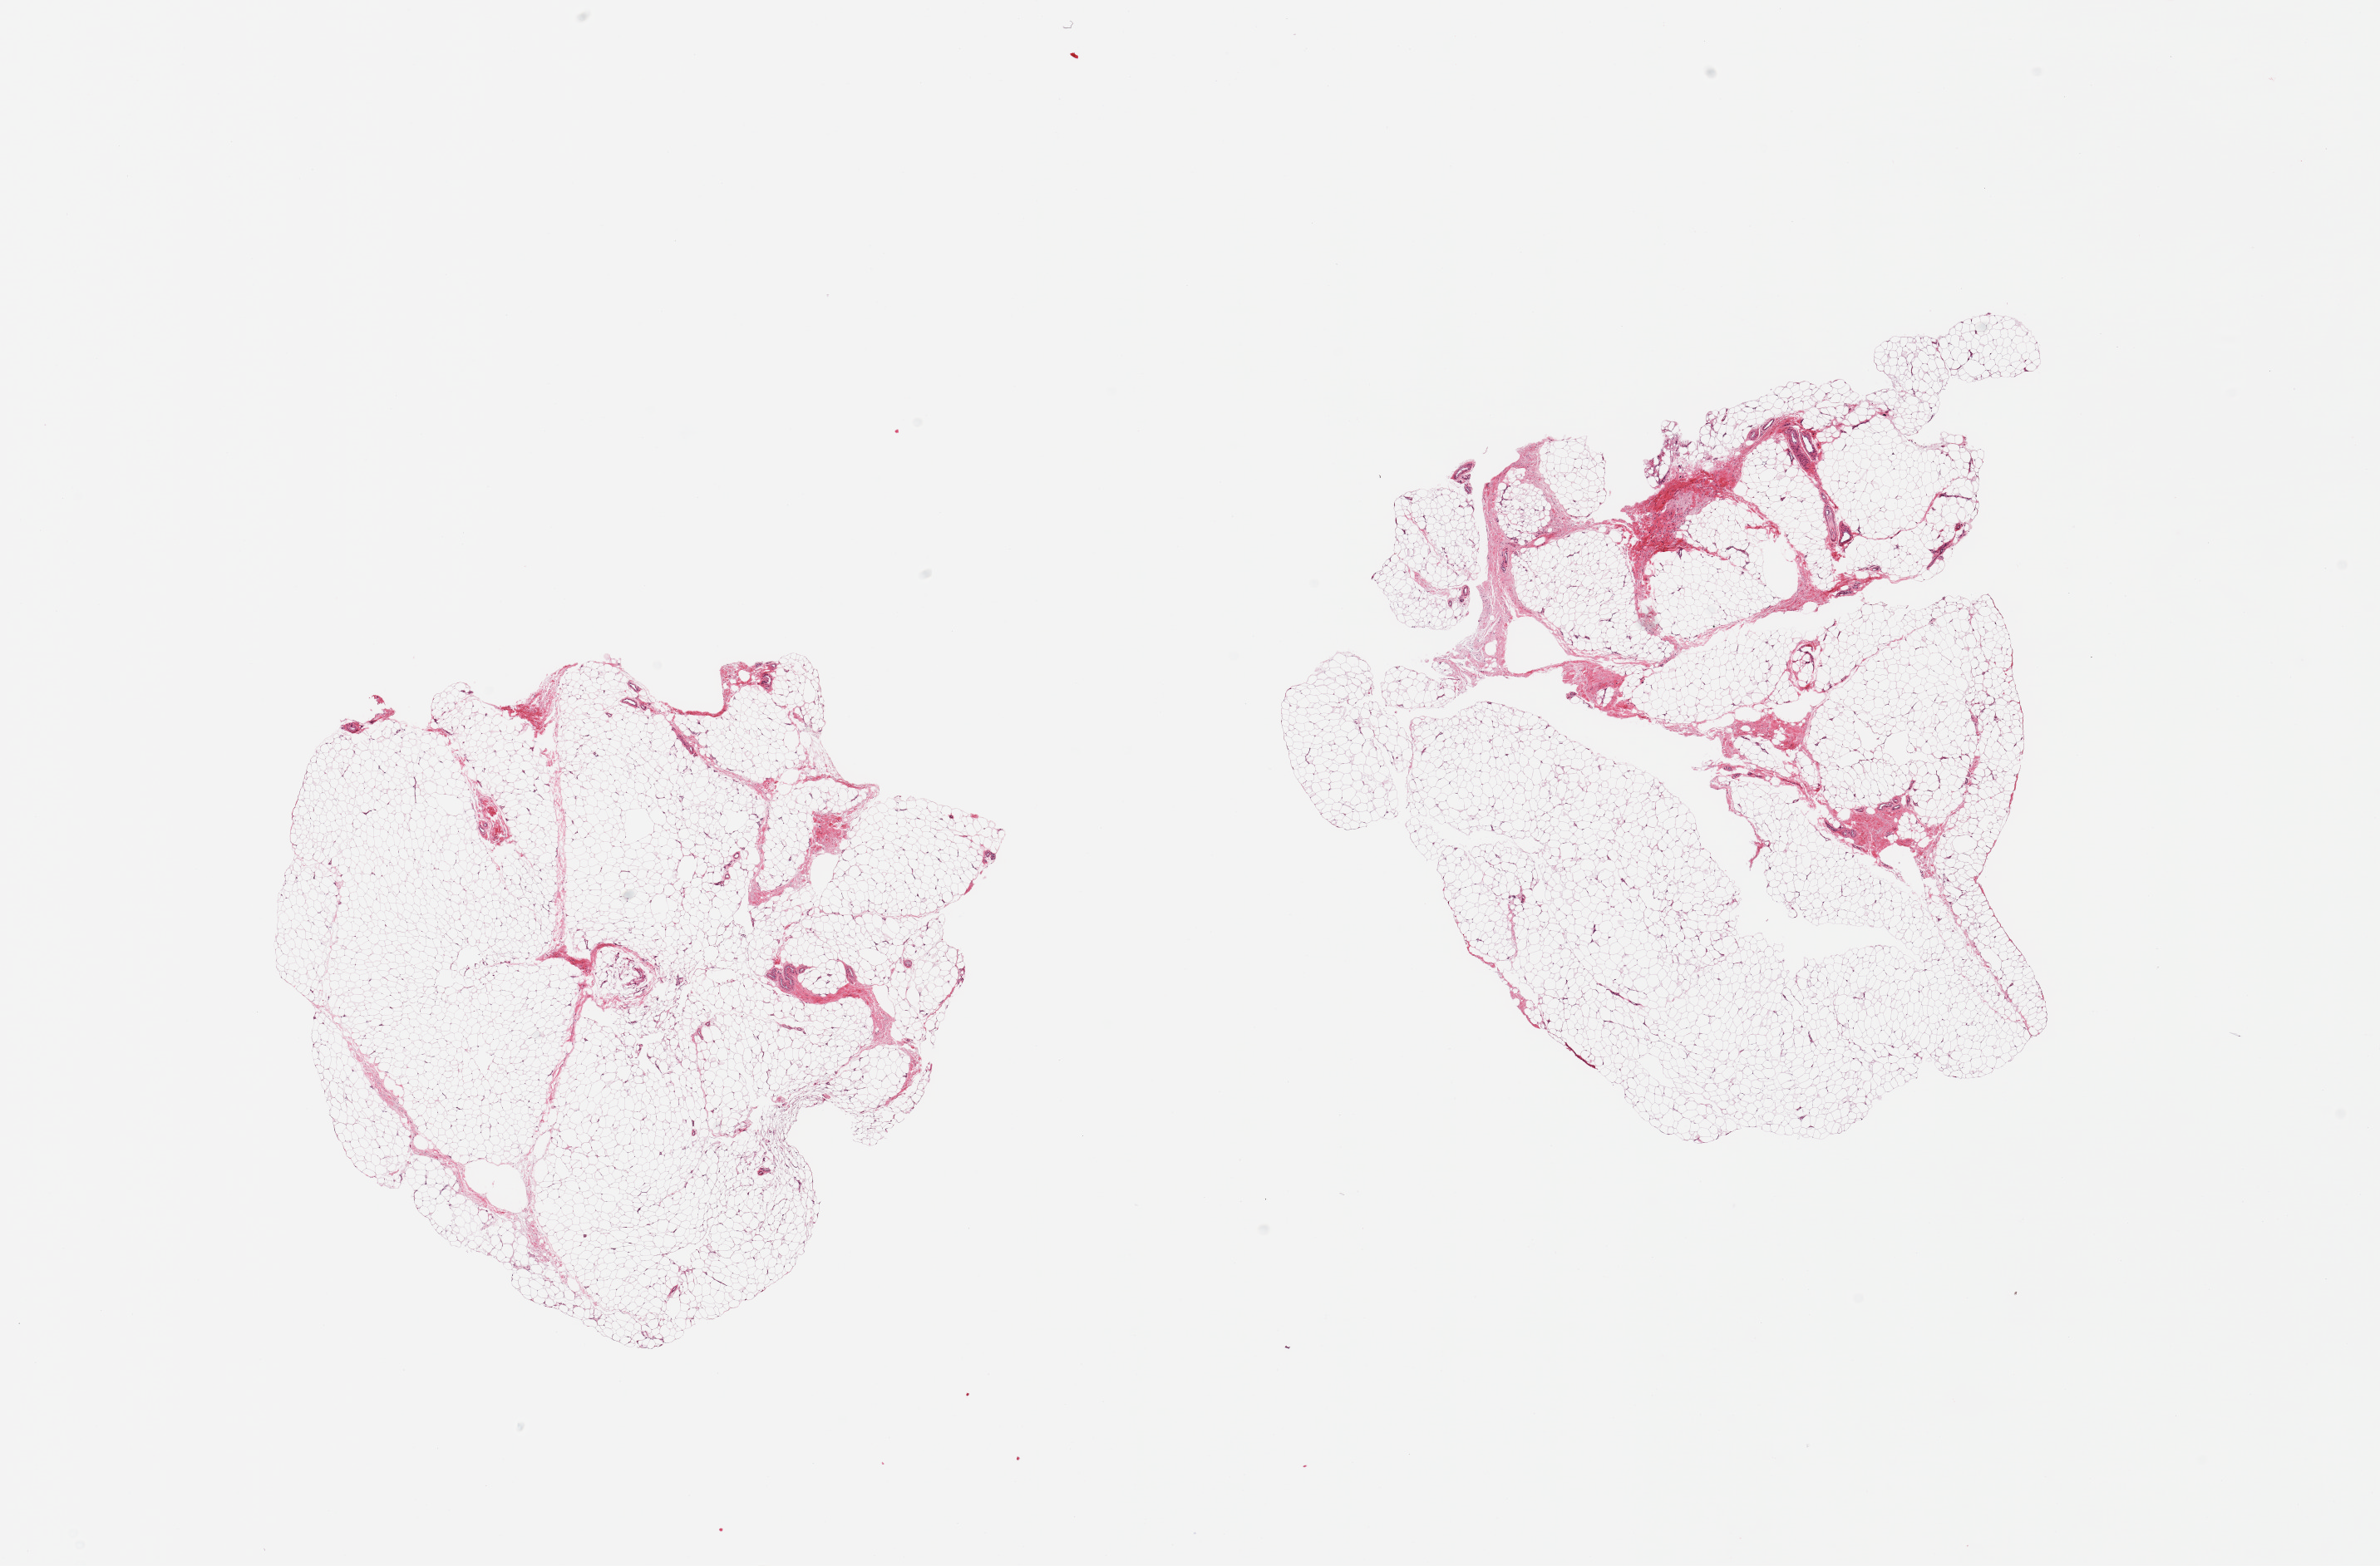
Hematoxylin and eosin (H&E) whole-slide image, brightfield — whole scanned area (about 22.6 x 14.9 mm) shown as a low-resolution overview. PAXgene-fixed, paraffin-embedded tissue. Section of adipose tissue (target tissue). Donor tissue sample. Donor: female.
• review note (as recorded): 2 pieces, fascia/vascular elements, 5-10% tissue